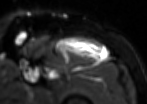
MRI of an extremity soft-tissue mass, one axial slice. Slice 75 of 85 in the series (ordered by position). T2-weighted fat-saturated. MR volume resampled by the dataset authors to the PET/CT grid (not the native acquisition matrix). 3.27 mm slice thickness. 147 × 104 image matrix. Male patient. From the clinical record (not read from this slice): histological type: extraskeletal osteosarcoma; grade: high; site of the primary tumour: thigh.
Outlined on this slice (expert contour drawn on MRI and transferred to this co-registered scan by the dataset authors):
- gross tumour volume (mass): bounding box (x1, y1, x2, y2) in pixels: (58, 37, 107, 61)